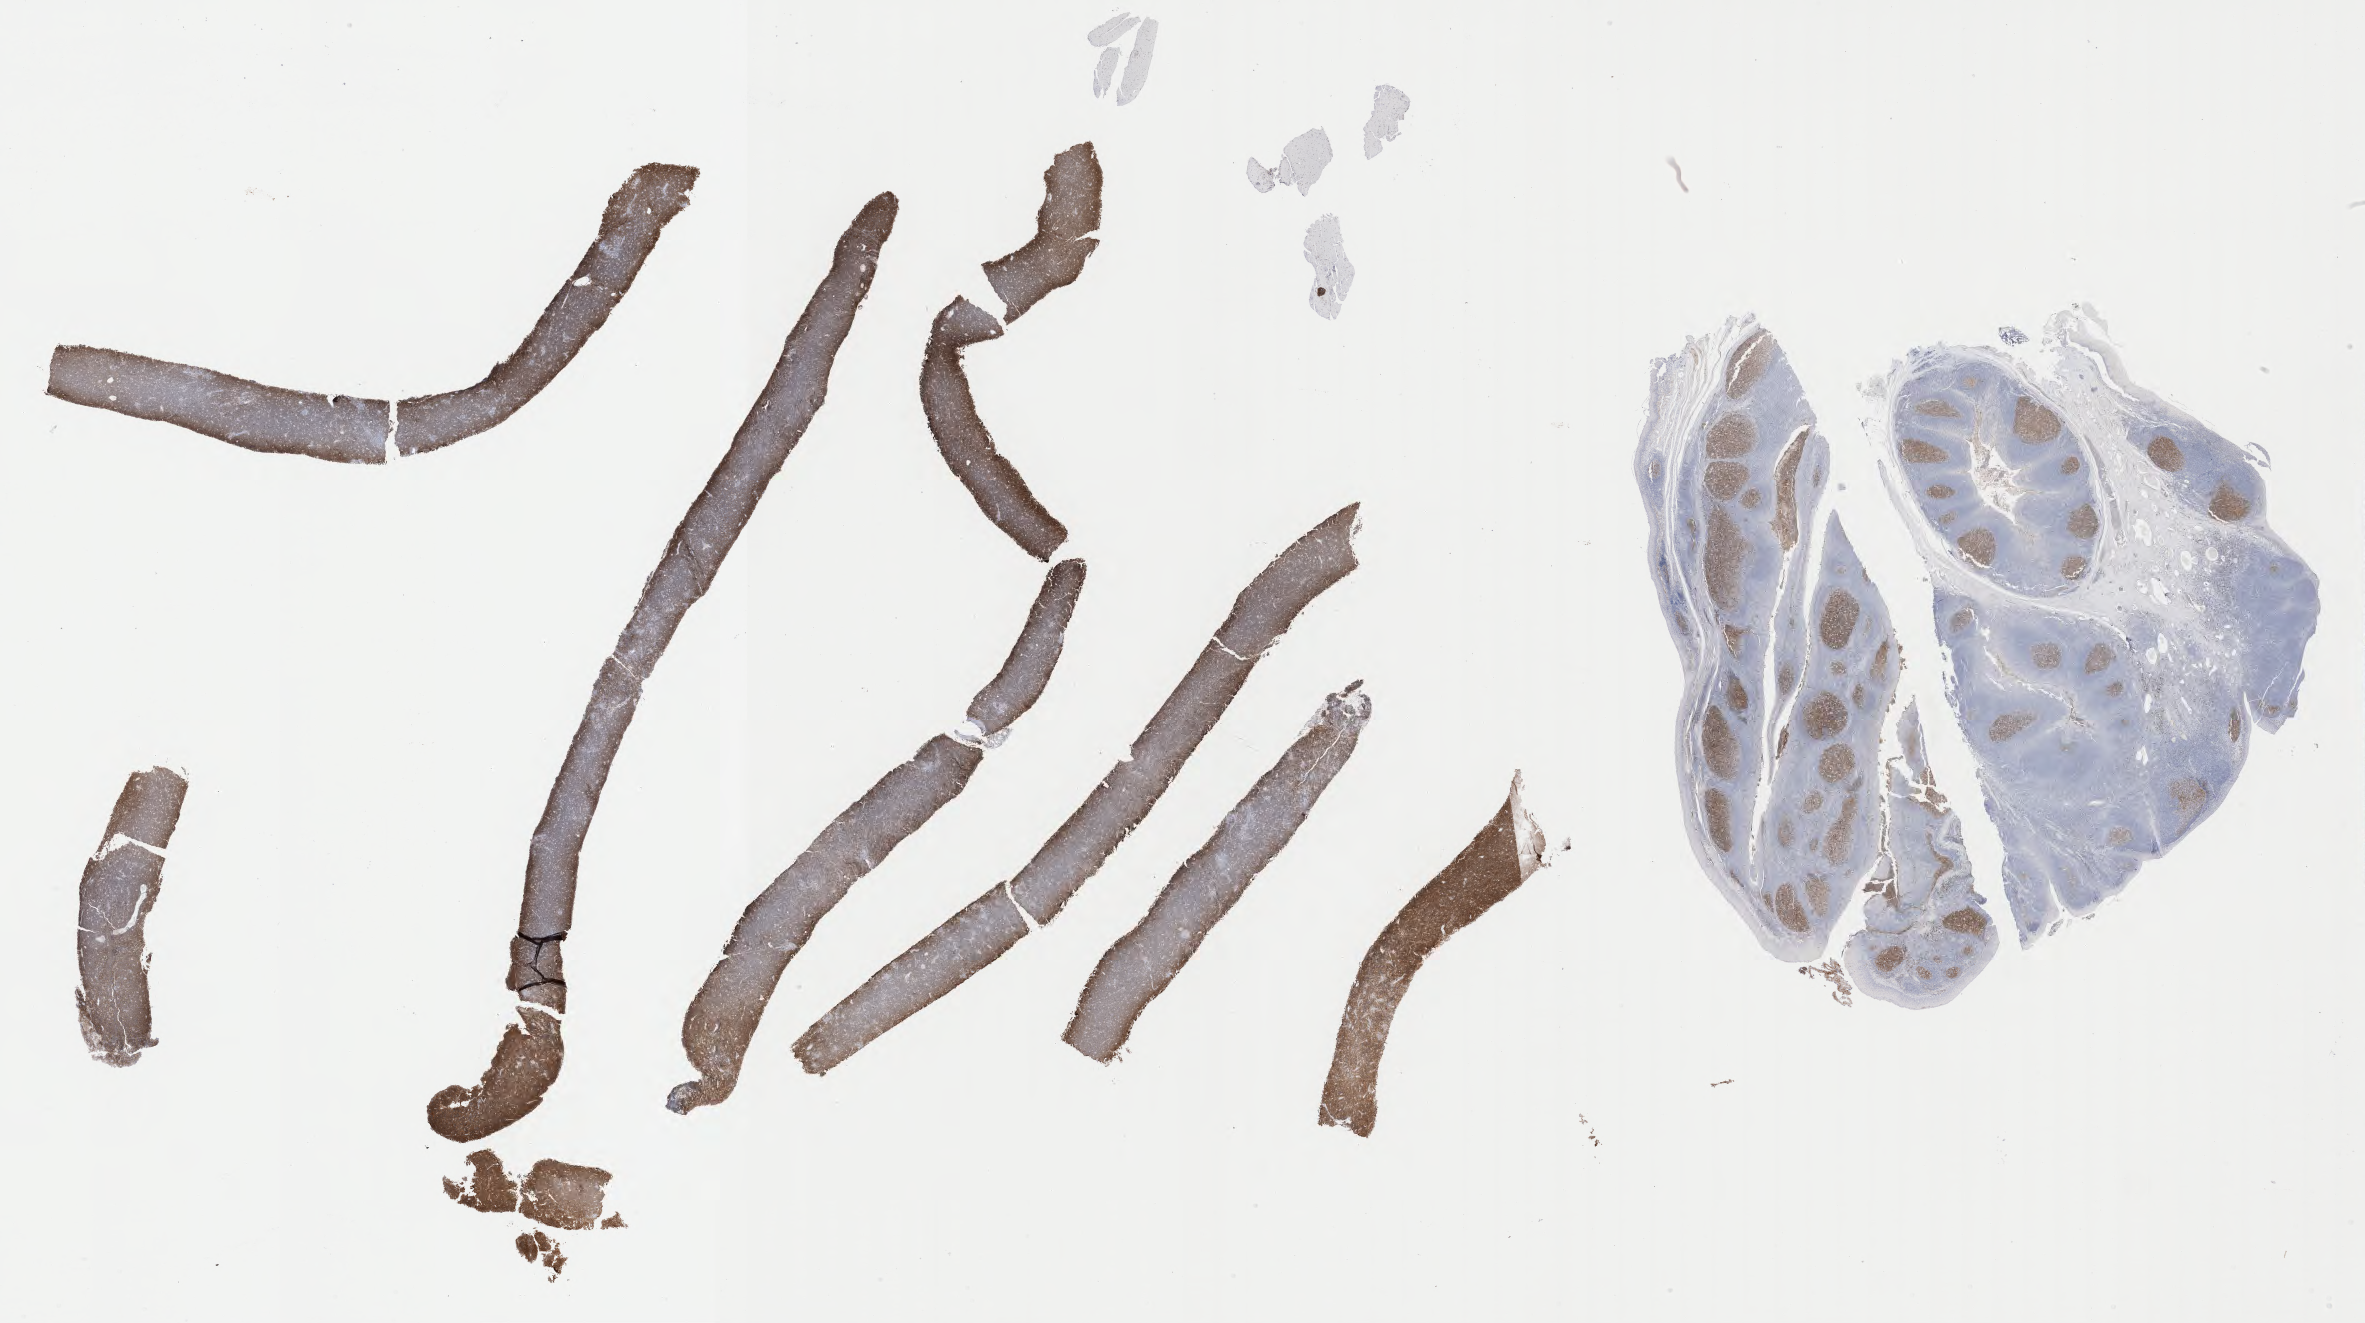
Immunohistochemistry (IHC) whole-slide image stained for CD10 — low-resolution overview of the scanned area, about 38.3 x 21.4 mm. Tumor tissue. Patient: male, aged 29.
Histologic diagnosis: Burkitt lymphoma, NOS.